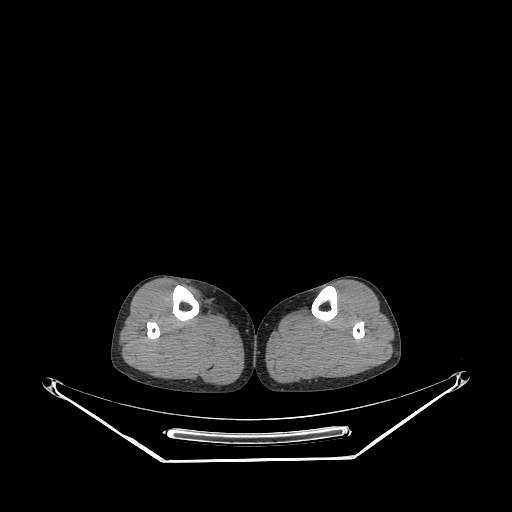
CT of an extremity soft-tissue mass (from a PET/CT study), one axial slice; slice 132 of 267 in the series (ordered by position); reconstruction kernel STANDARD; 140 kVp; soft-tissue window (W 400 / L 40 HU); 3.75 mm slice thickness; 512 × 512 image matrix, field of view 500 × 500 mm. Female patient. Case-level facts recorded for this patient, not image findings: histological type: undifferentiated – high grade; grade: high; site of the primary tumour: right thigh.
Structures marked on this image (expert contour drawn on MRI and transferred to this co-registered scan by the dataset authors):
- gross tumour volume (mass): bounding box [x1, y1, x2, y2] px = [187, 286, 204, 307]